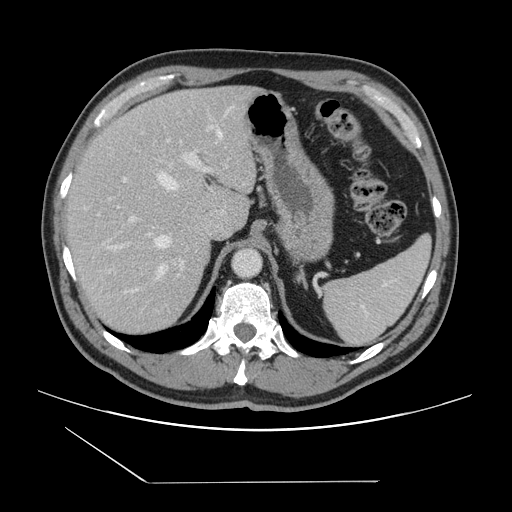
Contrast-enhanced abdominal CT, one axial slice. Intravenous contrast given. Soft-tissue window (W 400 / L 40 HU). 2.5 mm slice thickness. 512 × 512 image matrix, field of view 407 × 407 mm. Male patient, age 61 years. From the clinical record (not read from this slice): diagnosis: colorectal cancer liver metastases, imaged before liver resection; multiple liver metastases: yes; largest metastasis: 5.5 cm; disease in both lobes: yes.
Annotated regions visible in this slice (manually delineated by an expert):
- hepatic veins: bounding box <118,132,223,274> (left, top, right, bottom; pixels)
- liver: <68,86,258,335>
- planned liver remnant (the part of the liver to remain after resection): <68,86,238,229>
- portal vein (with intrahepatic branches): <109,126,211,268>